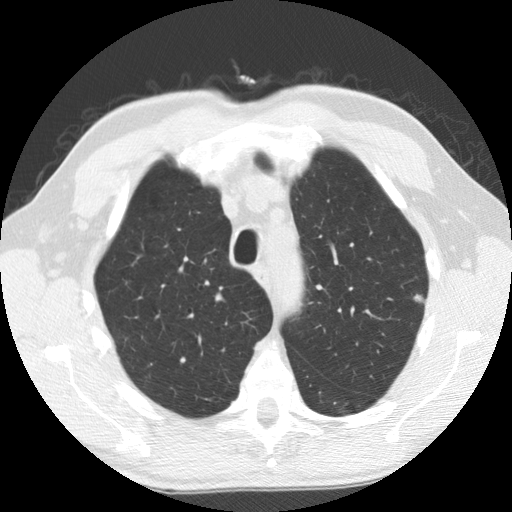
Low-dose screening chest CT, one axial slice. Position 129 of 158 along the scan axis. 120 kVp. Lung window (W 1500 / L -600 HU). 512 × 512 image matrix.
Annotated regions visible in this slice (outlined manually by an expert reader):
- lesion 1 (tumor, upper lobe of left lung): box from (x=414, y=294) to (x=426, y=305) px